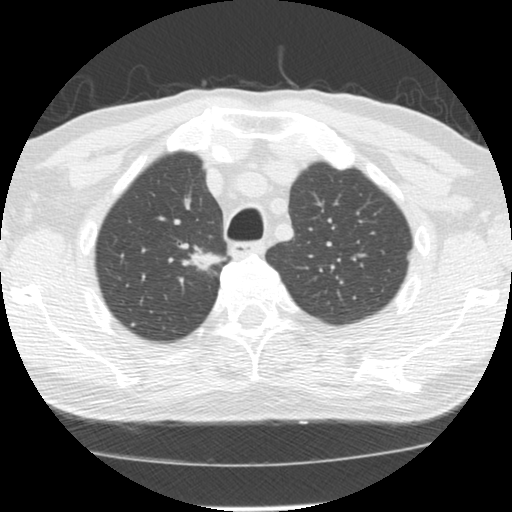
Low-dose screening chest CT, one axial slice; position 108 of 139 along the scan axis; 120 kVp; lung window (W 1500 / L -600 HU); 2.5 mm slice thickness; 512 × 512 image matrix, field of view 310 × 310 mm.
Outlined on this slice (outlined manually by an expert reader):
- lesion 1 (tumor, upper lobe of right lung): box from (x=182, y=248) to (x=226, y=274) px